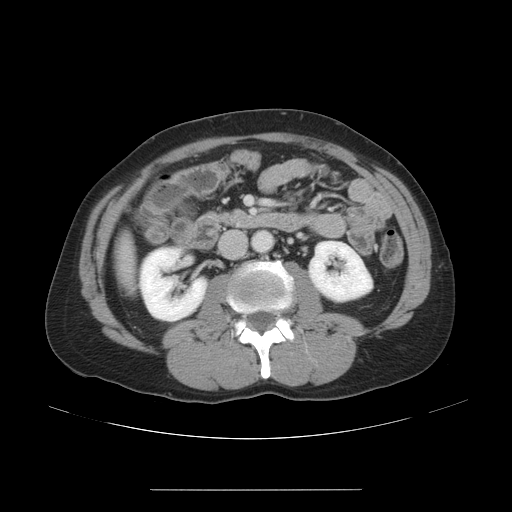
Contrast-enhanced abdominal CT, one axial slice. Slice 16 of 48 in the series (ordered by position). Intravenous contrast given. Soft-tissue window (W 400 / L 40 HU). 512 × 512 image matrix, field of view 409 × 409 mm. Male patient, age 56 years. From the clinical record (not read from this slice): diagnosis: colorectal cancer liver metastases, imaged before liver resection; multiple liver metastases: yes; largest metastasis: 1.8 cm; chemotherapy before resection: yes.
Outlined on this slice (expert manual segmentation):
- liver: bounding box [x1, y1, x2, y2] px = [121, 246, 132, 278]